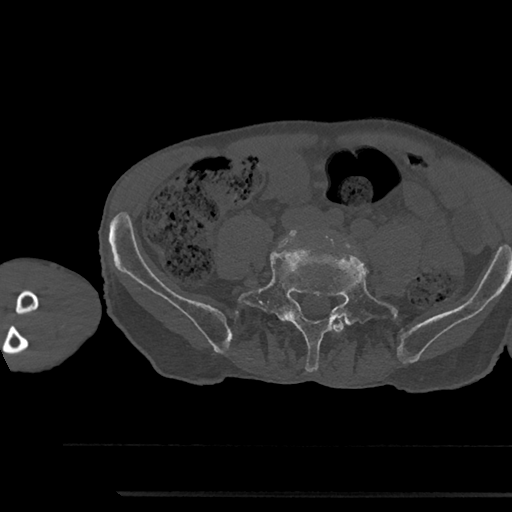
CT including the spine, one axial slice. Position 358 of 797 along the scan axis. Reconstruction kernel Br40s/3. 120 kVp. Bone window (W 1800 / L 400 HU). 0.5 mm slice thickness. 512 × 512 image matrix. Patient: male, 79 years. Case-level facts recorded for this patient, not image findings: primary cancer: prostate.
Annotated regions visible in this slice (semi-automatically segmented with operator editing):
- L4 vertebra: bounding box [x1, y1, x2, y2] px = [333, 320, 344, 333]
- L5 vertebra: [239, 250, 399, 372]